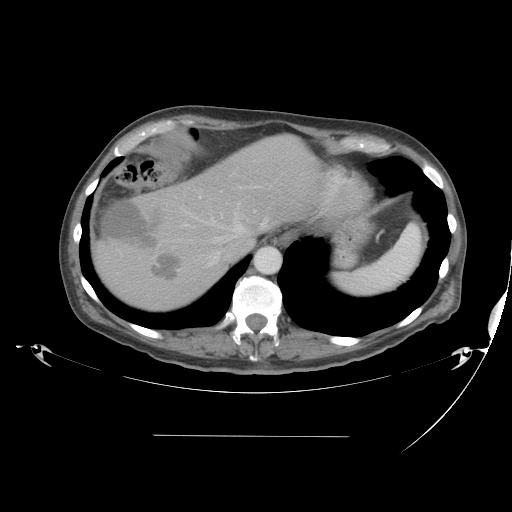
Contrast-enhanced abdominal CT, one axial slice; reconstruction kernel STANDARD; 120 kVp; intravenous contrast given; soft-tissue window (W 400 / L 40 HU); 5 mm slice thickness; 512 × 512 image matrix, field of view 486 × 486 mm. Male patient, age 65 years. From the clinical record (not read from this slice): diagnosis: colorectal cancer liver metastases, imaged before liver resection; multiple liver metastases: yes; largest metastasis: 11 cm.
Structures marked on this image (outlined manually by an expert reader):
- hepatic veins: bounding box <179,187,265,268> (left, top, right, bottom; pixels)
- liver: <92,136,323,313>
- planned liver remnant (the part of the liver to remain after resection): <179,135,323,237>
- portal vein (with intrahepatic branches): <180,190,255,229>
- liver metastasis: <152,253,179,279>
- liver metastasis: <103,202,162,249>